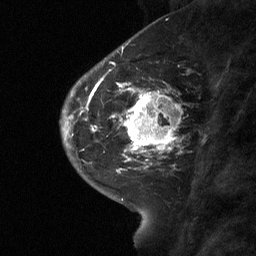
Breast MRI (dynamic contrast-enhanced), one sagittal slice. Position 23 of 64 along the scan axis. Dynamic contrast-enhanced study with each time point stored as its own series, time point 2 of 3 at this slice position (early post-contrast, ordered by acquisition time). 1.5 T. TE 4.8 ms, TR 27 ms. 2 mm slice thickness. 256 × 256 image matrix, field of view 180 × 180 mm. Patient: female, 42 years. Case-level facts recorded for this patient, not image findings: setting: breast cancer imaged before/during neoadjuvant chemotherapy; receptor status: triple-negative.
Outlined on this slice (semi-automatic segmentation, software-assisted and operator-edited):
- analysis volume of interest (the breast-tissue region the enhancement analysis was run in; not a lesion): bounding box (x1, y1, x2, y2) in pixels: (115, 85, 180, 160)
- tumour enhancement mask (voxels above the 90 % enhancement threshold inside the analysis volume of interest): (115, 85, 175, 160)